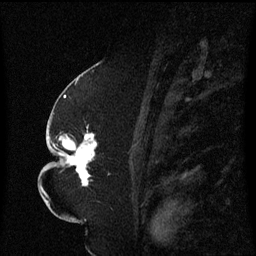
Breast MRI (dynamic contrast-enhanced), one sagittal slice. Position 34 of 60 along the scan axis. Dynamic contrast-enhanced series, image 2 of 3 at this slice position (ordered by acquisition). 1.5 T. TE 4.2 ms, TR 8.4 ms. 2.3 mm slice thickness. 256 × 256 image matrix, field of view 200 × 200 mm. Female patient, age 52 years. Case-level facts recorded for this patient, not image findings: setting: breast cancer imaged before/during neoadjuvant chemotherapy; receptor status: HR-positive, HER2-negative.
Annotated regions visible in this slice (semi-automatically segmented with operator editing):
- analysis volume of interest (the breast-tissue region the enhancement analysis was run in; not a lesion): bounding box (x1, y1, x2, y2) in pixels: (49, 124, 111, 187)
- tumour enhancement mask (voxels above the 70 % enhancement threshold inside the analysis volume of interest): (52, 134, 97, 187)